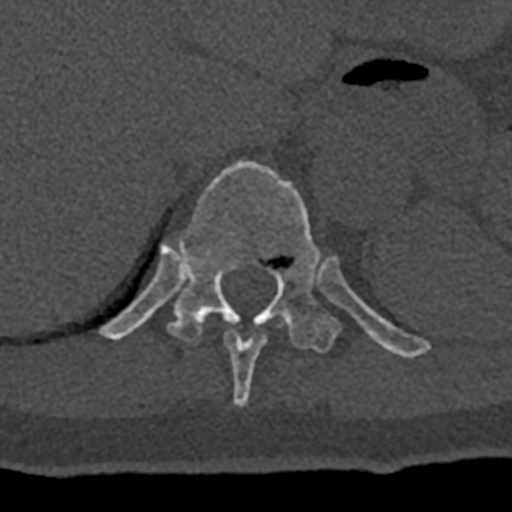
CT including the spine, one axial slice; position 565 of 797 along the scan axis; bone window (W 1800 / L 400 HU); 0.5 mm slice thickness; 512 × 512 image matrix, field of view 160 × 160 mm. Patient: male, 74 years. From the clinical record (not read from this slice): primary cancer: renal.
Annotated regions visible in this slice (semi-automatically segmented with operator editing):
- T10 vertebra: bounding box [x1, y1, x2, y2] px = [223, 330, 268, 406]
- T11 vertebra: [100, 159, 430, 358]